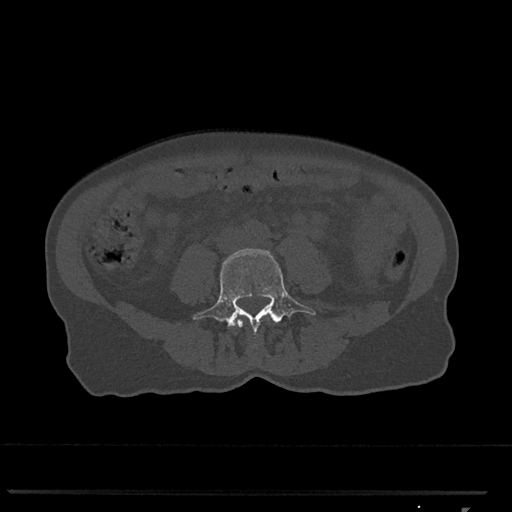
CT including the spine, one axial slice. Position 219 of 793 along the scan axis. Reconstruction kernel Br40s/3. Bone window (W 1800 / L 400 HU). 0.5 mm slice thickness. 512 × 512 image matrix, field of view 380 × 380 mm. Patient: female, 62 years. From the clinical record (not read from this slice): primary cancer: renal.
Outlined on this slice (semi-automatically segmented with operator editing):
- L3 vertebra: bounding box [x1, y1, x2, y2] px = [235, 319, 242, 326]
- L4 vertebra: [193, 248, 316, 332]